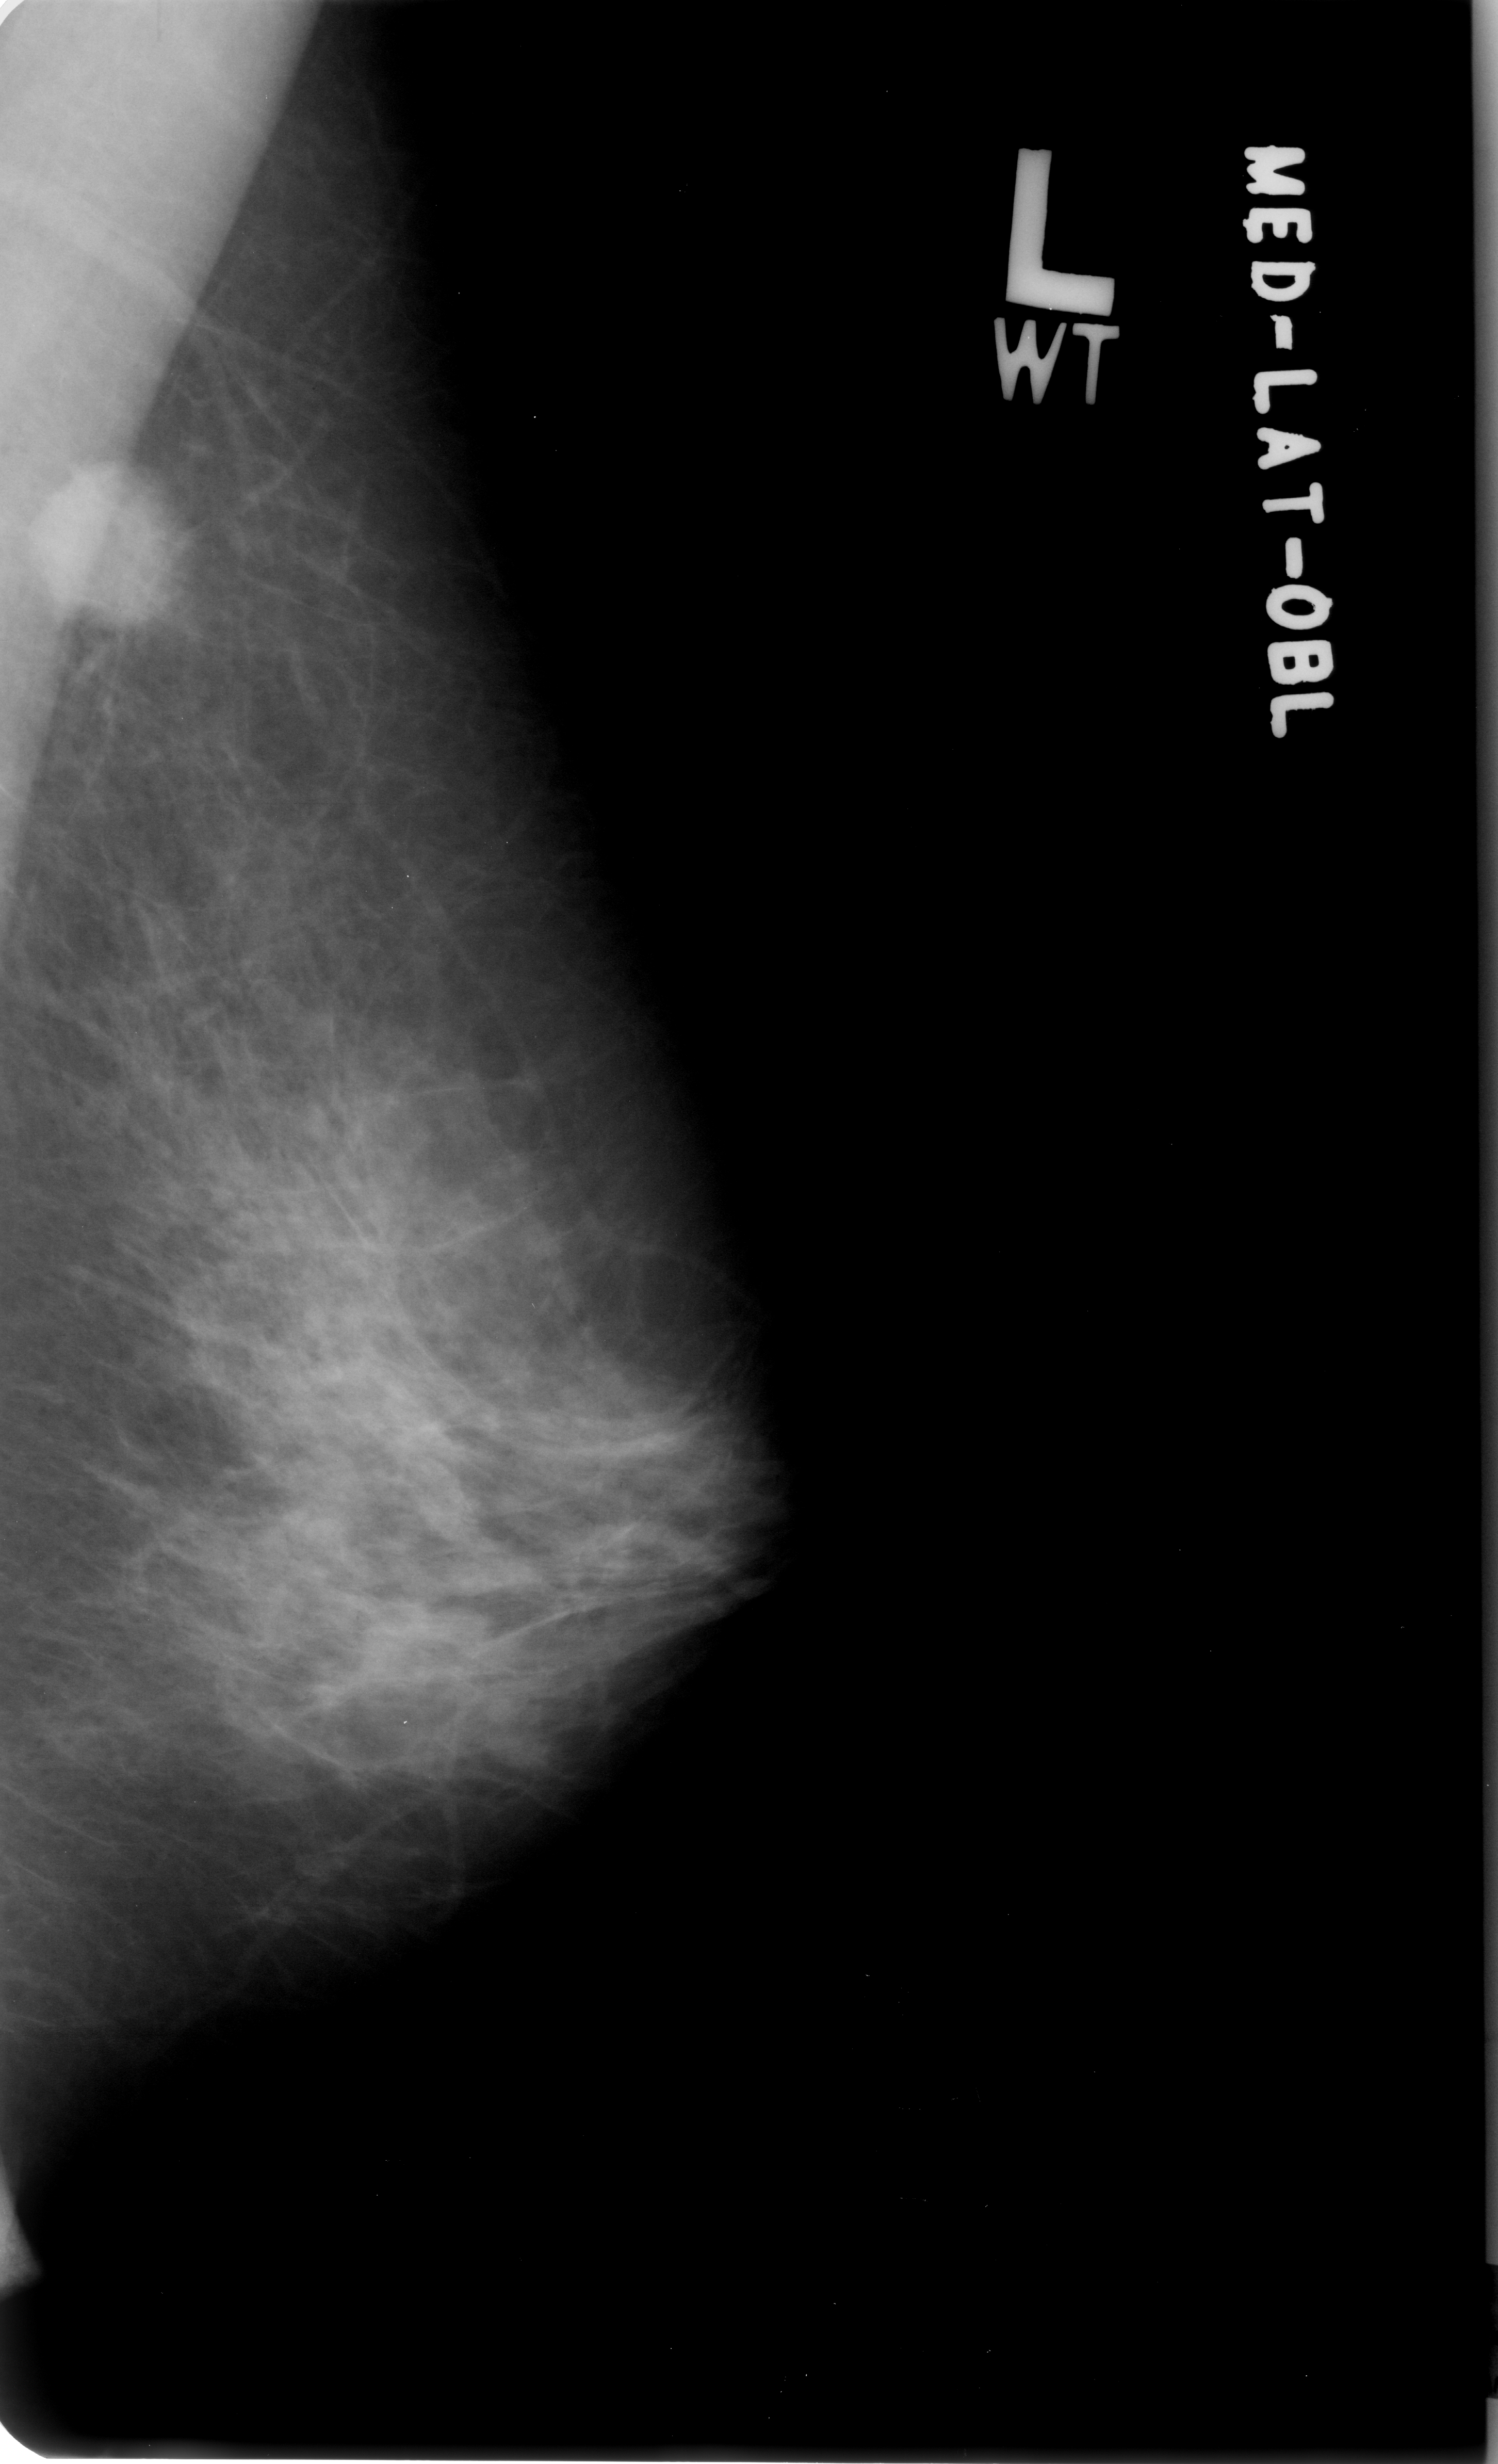
Mammogram (digitized film), left breast, mediolateral oblique (MLO) view, breast composition: heterogeneously dense (BI-RADS density category 3 of 4).
Finding: mass, shape round, margins ill defined; BI-RADS assessment category 4; pathology result (as recorded, not read from the image): malignant.